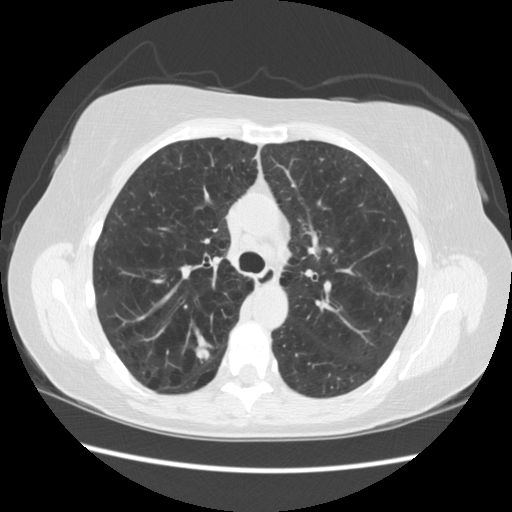
Low-dose screening chest CT, one axial slice; slice 157 of 235 in the series (ordered by position); reconstruction kernel STANDARD; lung window (W 1500 / L -600 HU); 2.5 mm slice thickness; 512 × 512 image matrix.
Annotated regions visible in this slice (outlined manually by an expert reader):
- lesion 1 (tumor, upper lobe of right lung): bounding box (x1, y1, x2, y2) in pixels: (196, 350, 209, 363)